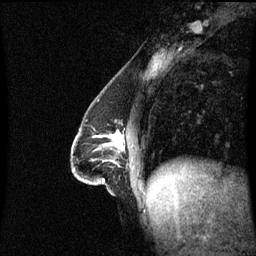
Breast MRI (dynamic contrast-enhanced), one sagittal slice; dynamic contrast-enhanced series, image 2 of 3 at this slice position (ordered by acquisition); 1.5 T; TE 4.2 ms, TR 8.9 ms; 2.2 mm slice thickness; 256 × 256 image matrix, field of view 210 × 210 mm. Female patient, age 47 years. Case-level facts recorded for this patient, not image findings: setting: breast cancer imaged before/during neoadjuvant chemotherapy; receptor status: HR-positive, HER2-negative.
Outlined on this slice (semi-automatically segmented with operator editing):
- analysis volume of interest (the breast-tissue region the enhancement analysis was run in; not a lesion): bounding box <72,129,122,195> (left, top, right, bottom; pixels)
- tumour enhancement mask (voxels above the 70 % enhancement threshold inside the analysis volume of interest): <116,133,120,148>